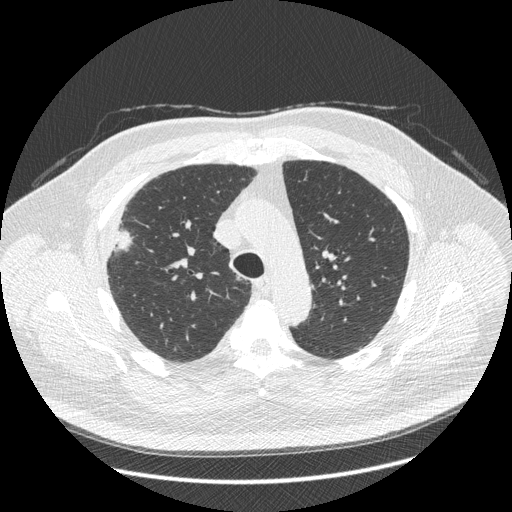
Chest CT (low-dose screening protocol), one axial image. Third screening round (two years after baseline). Lung window (W 1500 / L -600 HU). 1.25 mm slice thickness. Slice 115 of 426 in the series. Male participant, aged 66 years at enrolment. Current smoker at enrolment.
- Expert reader's lesion annotation, bounding box <88,209,148,271> (left, top, right, bottom; pixels).
- Screening reader's record for this exam (one nodule recorded; not confirmed to be the boxed lesion): non-calcified nodule or mass ≥4 mm, right upper lobe, 48 × 25 mm, spiculated (stellate) margins, soft tissue attenuation, pre-existing on the prior screen: no.
- Official screen result: positive, other.
- Later outcome: lung cancer diagnosed 35 days after this screen — non-small cell carcinoma, right upper lobe, stage IV (AJCC 6th edition), 50 mm at pathology.